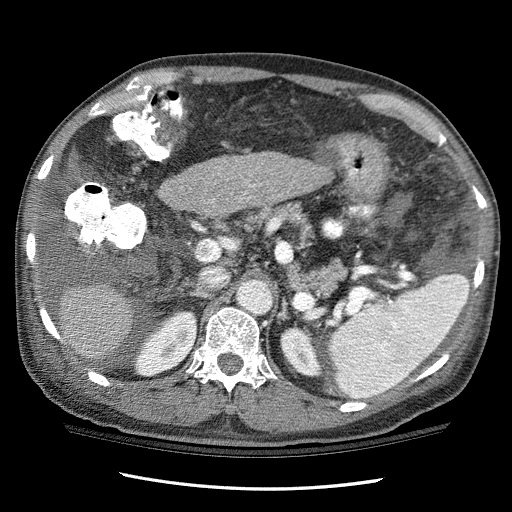
Contrast-enhanced abdominal CT (liver protocol), one axial slice; position 60 of 114 along the scan axis; 120 kVp; one of 3 acquisitions stored at this slice position; soft-tissue window (W 400 / L 40 HU); 2.5 mm slice thickness; 512 × 512 image matrix, field of view 360 × 360 mm. Case-level facts recorded for this patient, not image findings: diagnosis: hepatocellular carcinoma (patient treated with transarterial chemoembolisation; whether this scan precedes or follows treatment is not stated here); TNM stage (as recorded): Stage-I; Child-Pugh class: C; tumour differentiation: well differentiated.
Outlined on this slice (semi-automatically segmented with operator editing):
- liver parenchyma outside the tumour (the mass and vessels are separate outlines, so this box may not span the whole liver): bounding box (x1, y1, x2, y2) in pixels: (58, 152, 332, 364)